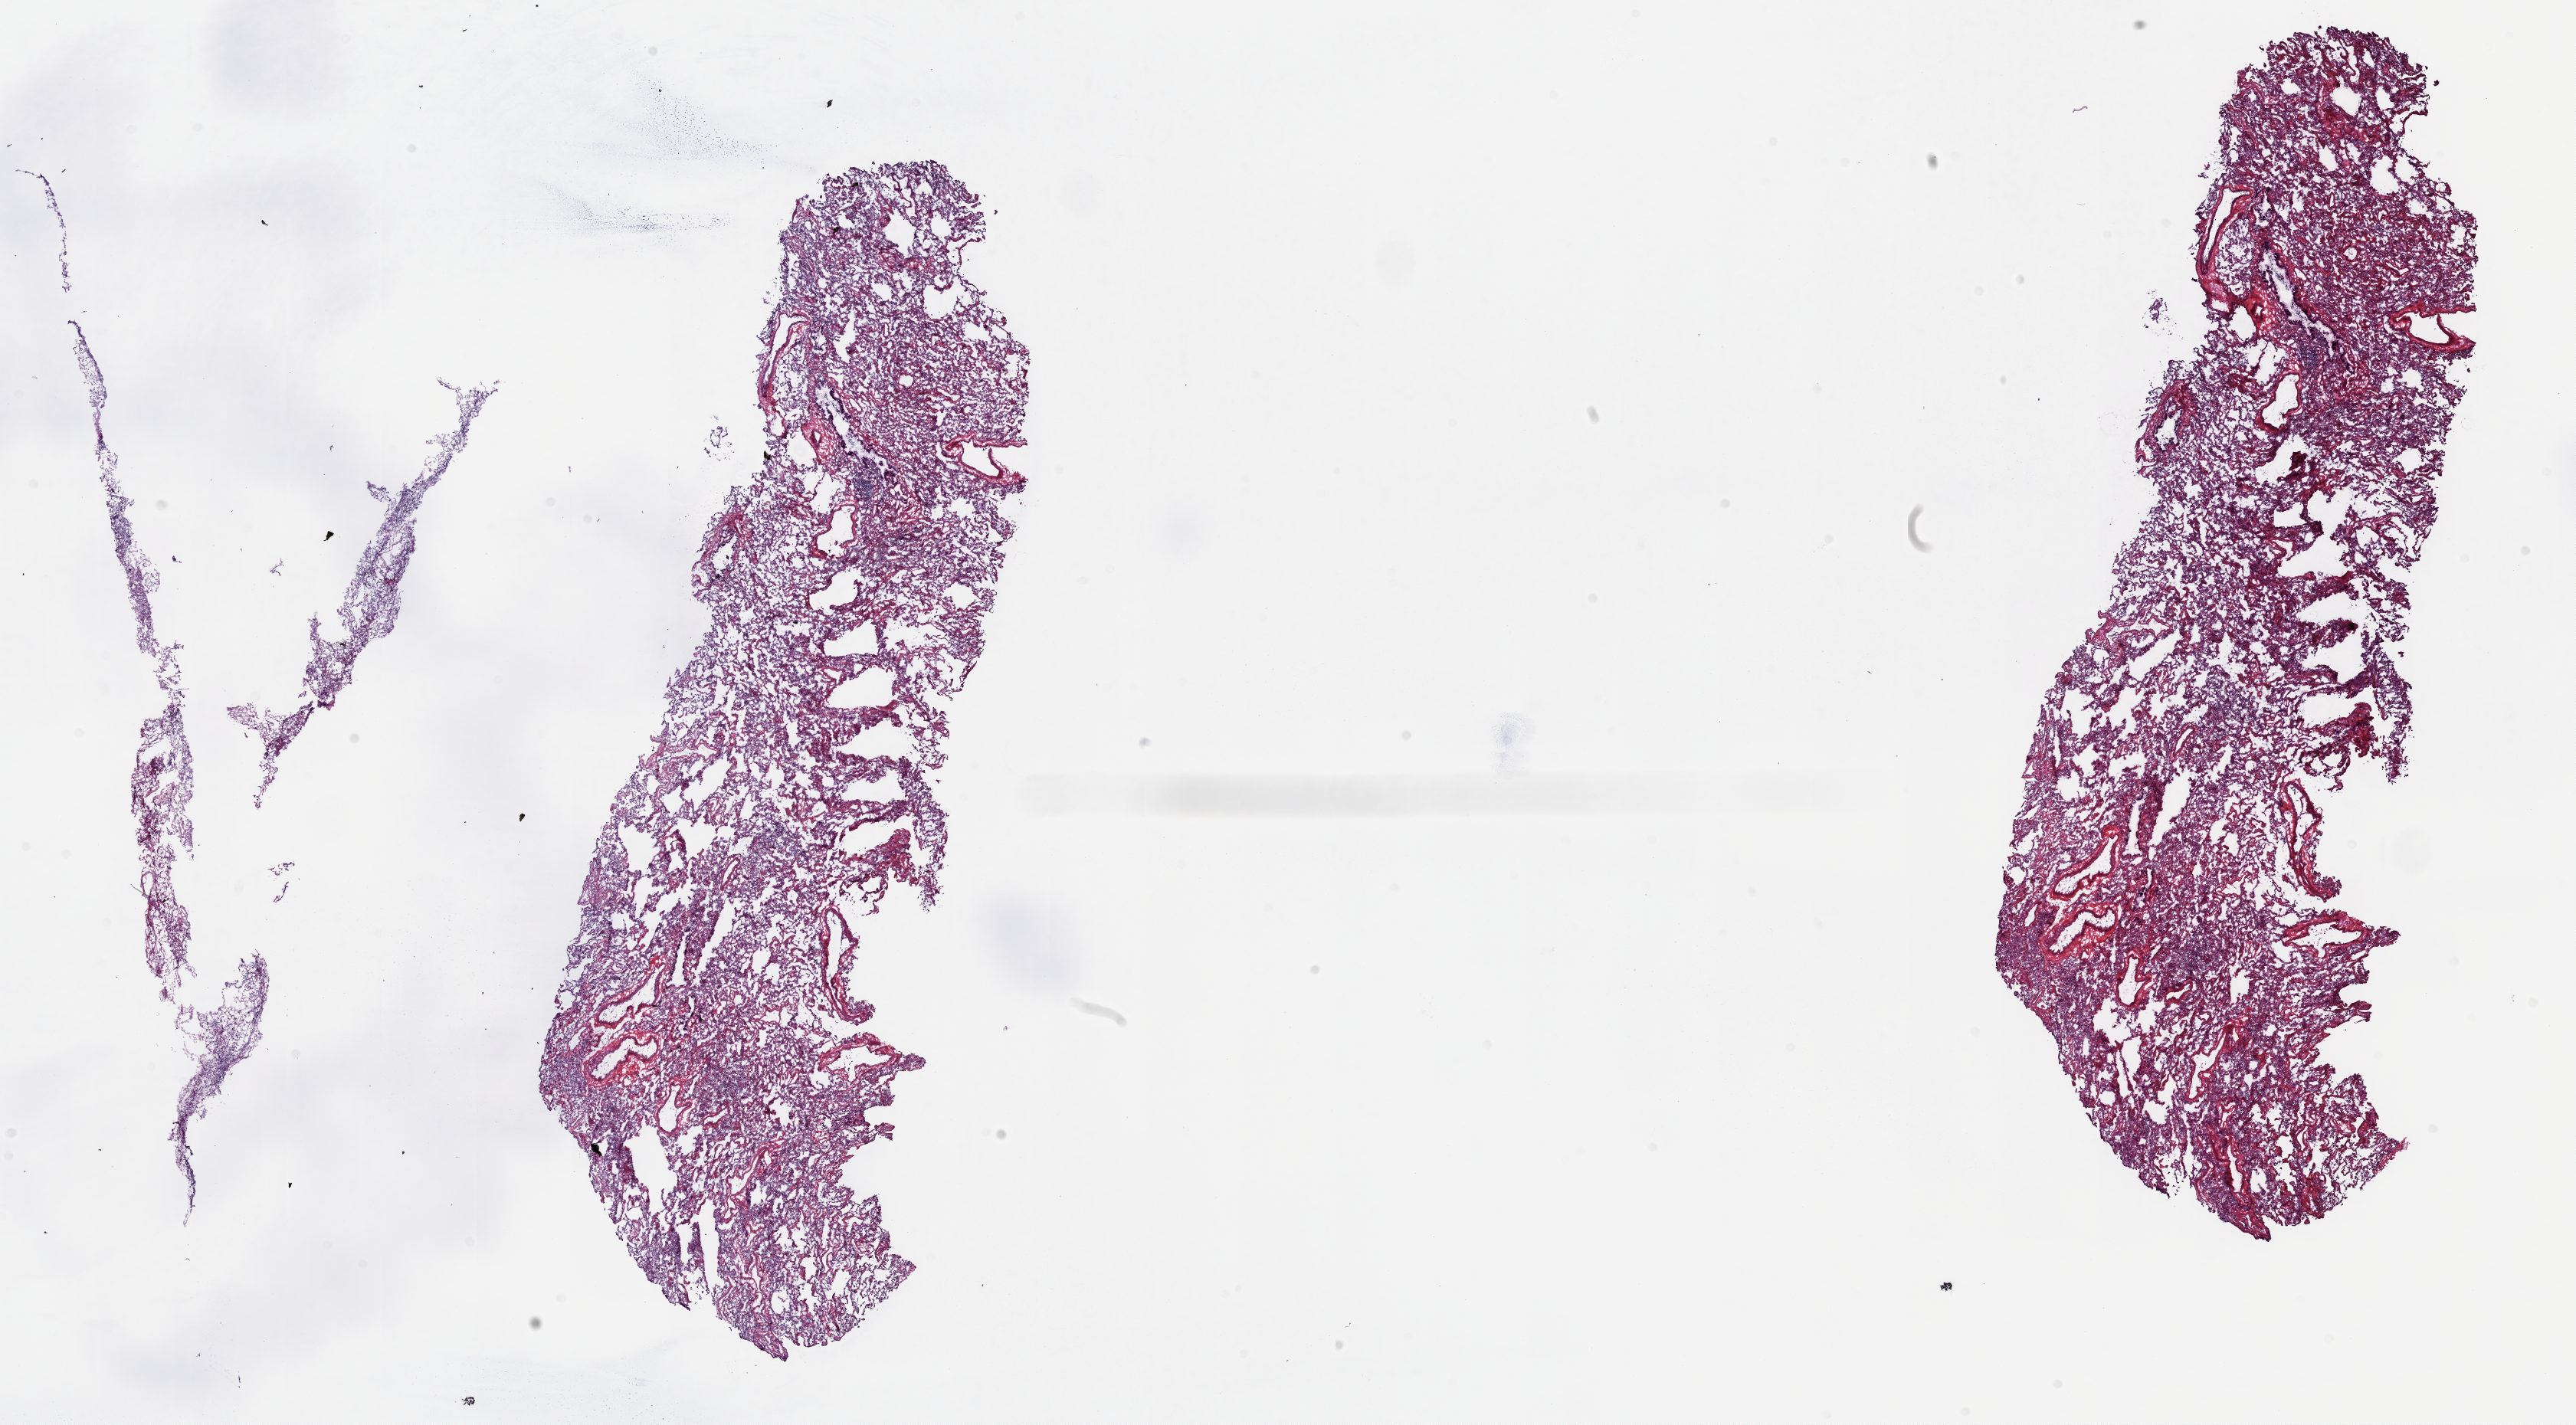
Digitized H&E tissue section (whole slide), low-resolution overview of the scanned area, about 27.1 x 15.0 mm (from a 20x scan). Frozen section. Lung, solid tissue normal (non-tumour tissue) sample. Female patient; age at initial diagnosis 56 years. Composition of this section per pathologist review: tumour cells 0%, tumour nuclei 0%, normal cells 50%, stromal cells 50%, necrosis 0%. Infiltration values recorded for this section: lymphocyte infiltration 10%, monocyte infiltration 10%, neutrophil infiltration 0%.
• this section: solid tissue normal (non-tumour) sample from the same patient
• patient diagnosis: Adenocarcinoma, NOS (lower lobe, lung)